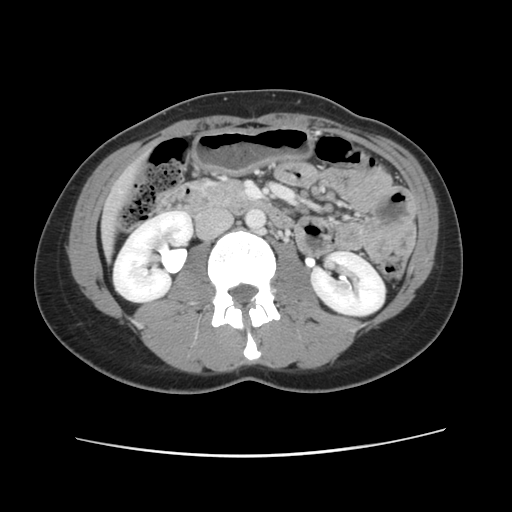
Contrast-enhanced abdominal CT, one axial slice; slice 24 of 134 in the series (ordered by position); intravenous contrast given; soft-tissue window (W 400 / L 40 HU); 512 × 512 image matrix, field of view 339 × 339 mm. Female patient, age 33 years. From the clinical record (not read from this slice): diagnosis: colorectal cancer liver metastases, imaged before liver resection; multiple liver metastases: yes; largest metastasis: 4.5 cm; chemotherapy before resection: no.
Outlined on this slice (expert manual segmentation):
- liver: bounding box <101,161,142,256> (left, top, right, bottom; pixels)